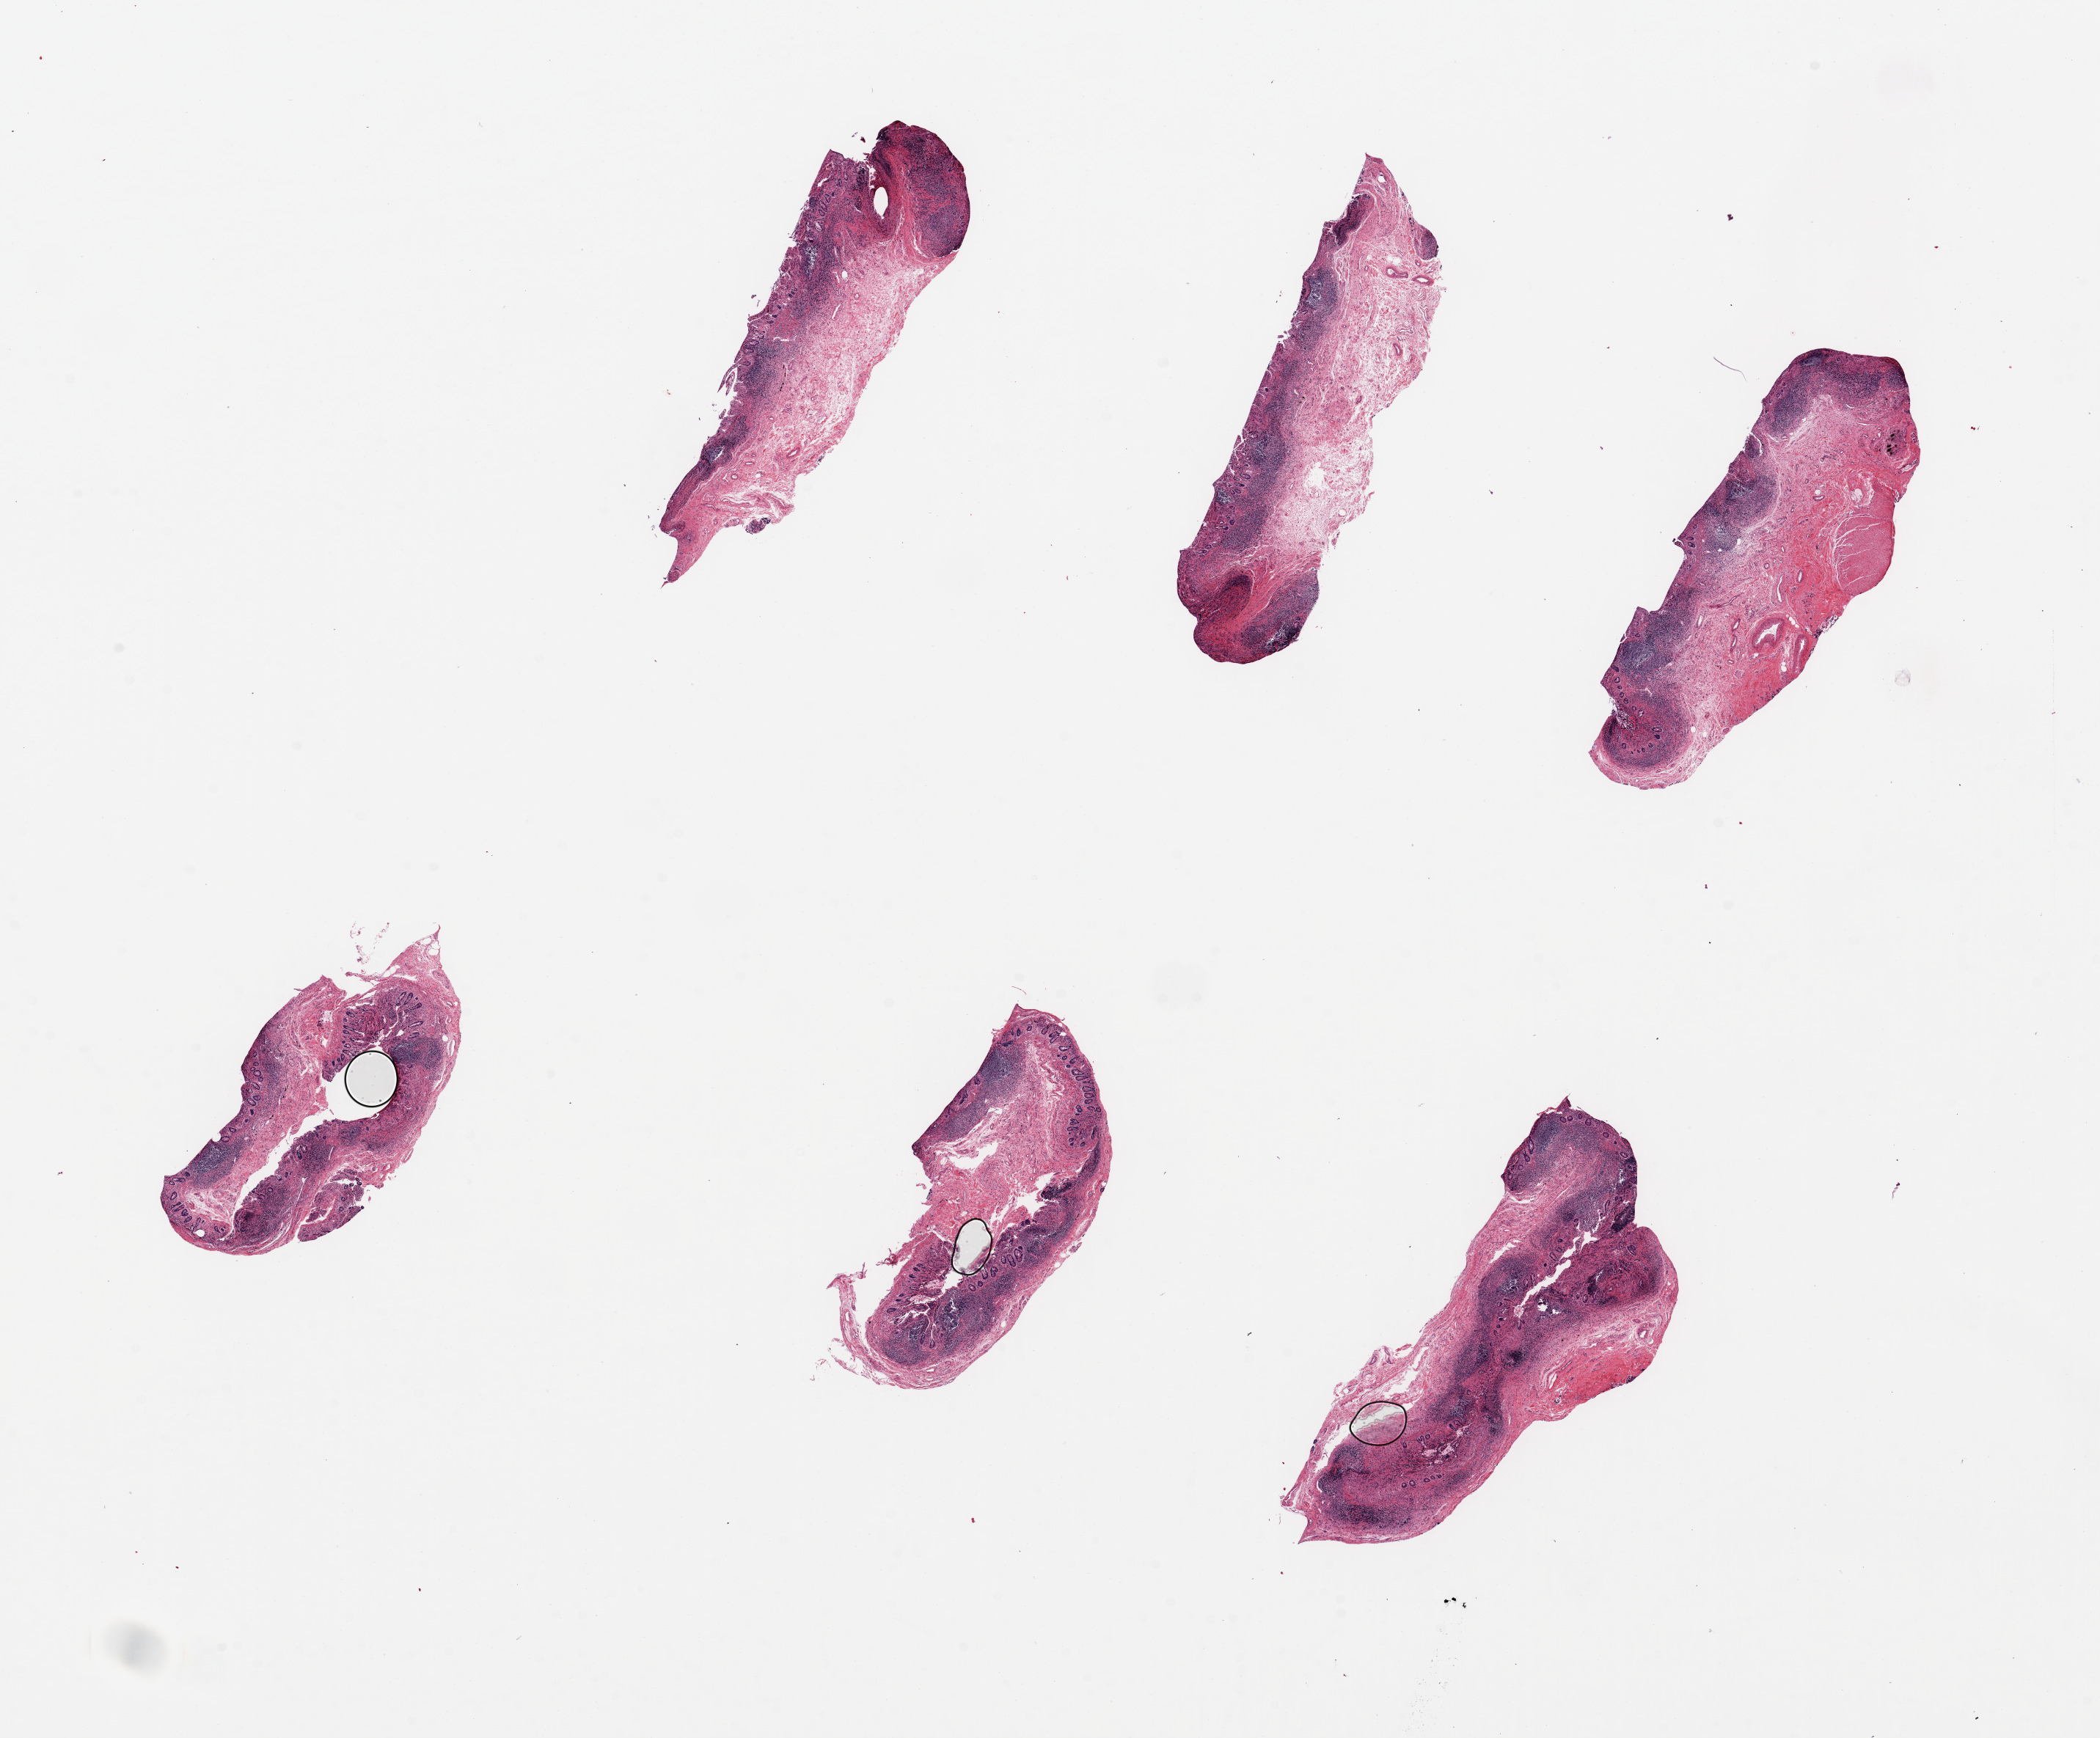
Haematoxylin and eosin whole-slide image, brightfield — whole scanned area (about 22.6 x 18.7 mm) shown as a low-resolution overview; PAXgene-fixed, paraffin-embedded tissue; sampled site (target tissue): ileum; donor tissue sample. Male donor.
* pathologist's review note for this sample: 6 pieces, ~7x1.5mm. Lymphoid elements present to a depth of ~0.5mm or ~30%, muscularis still present